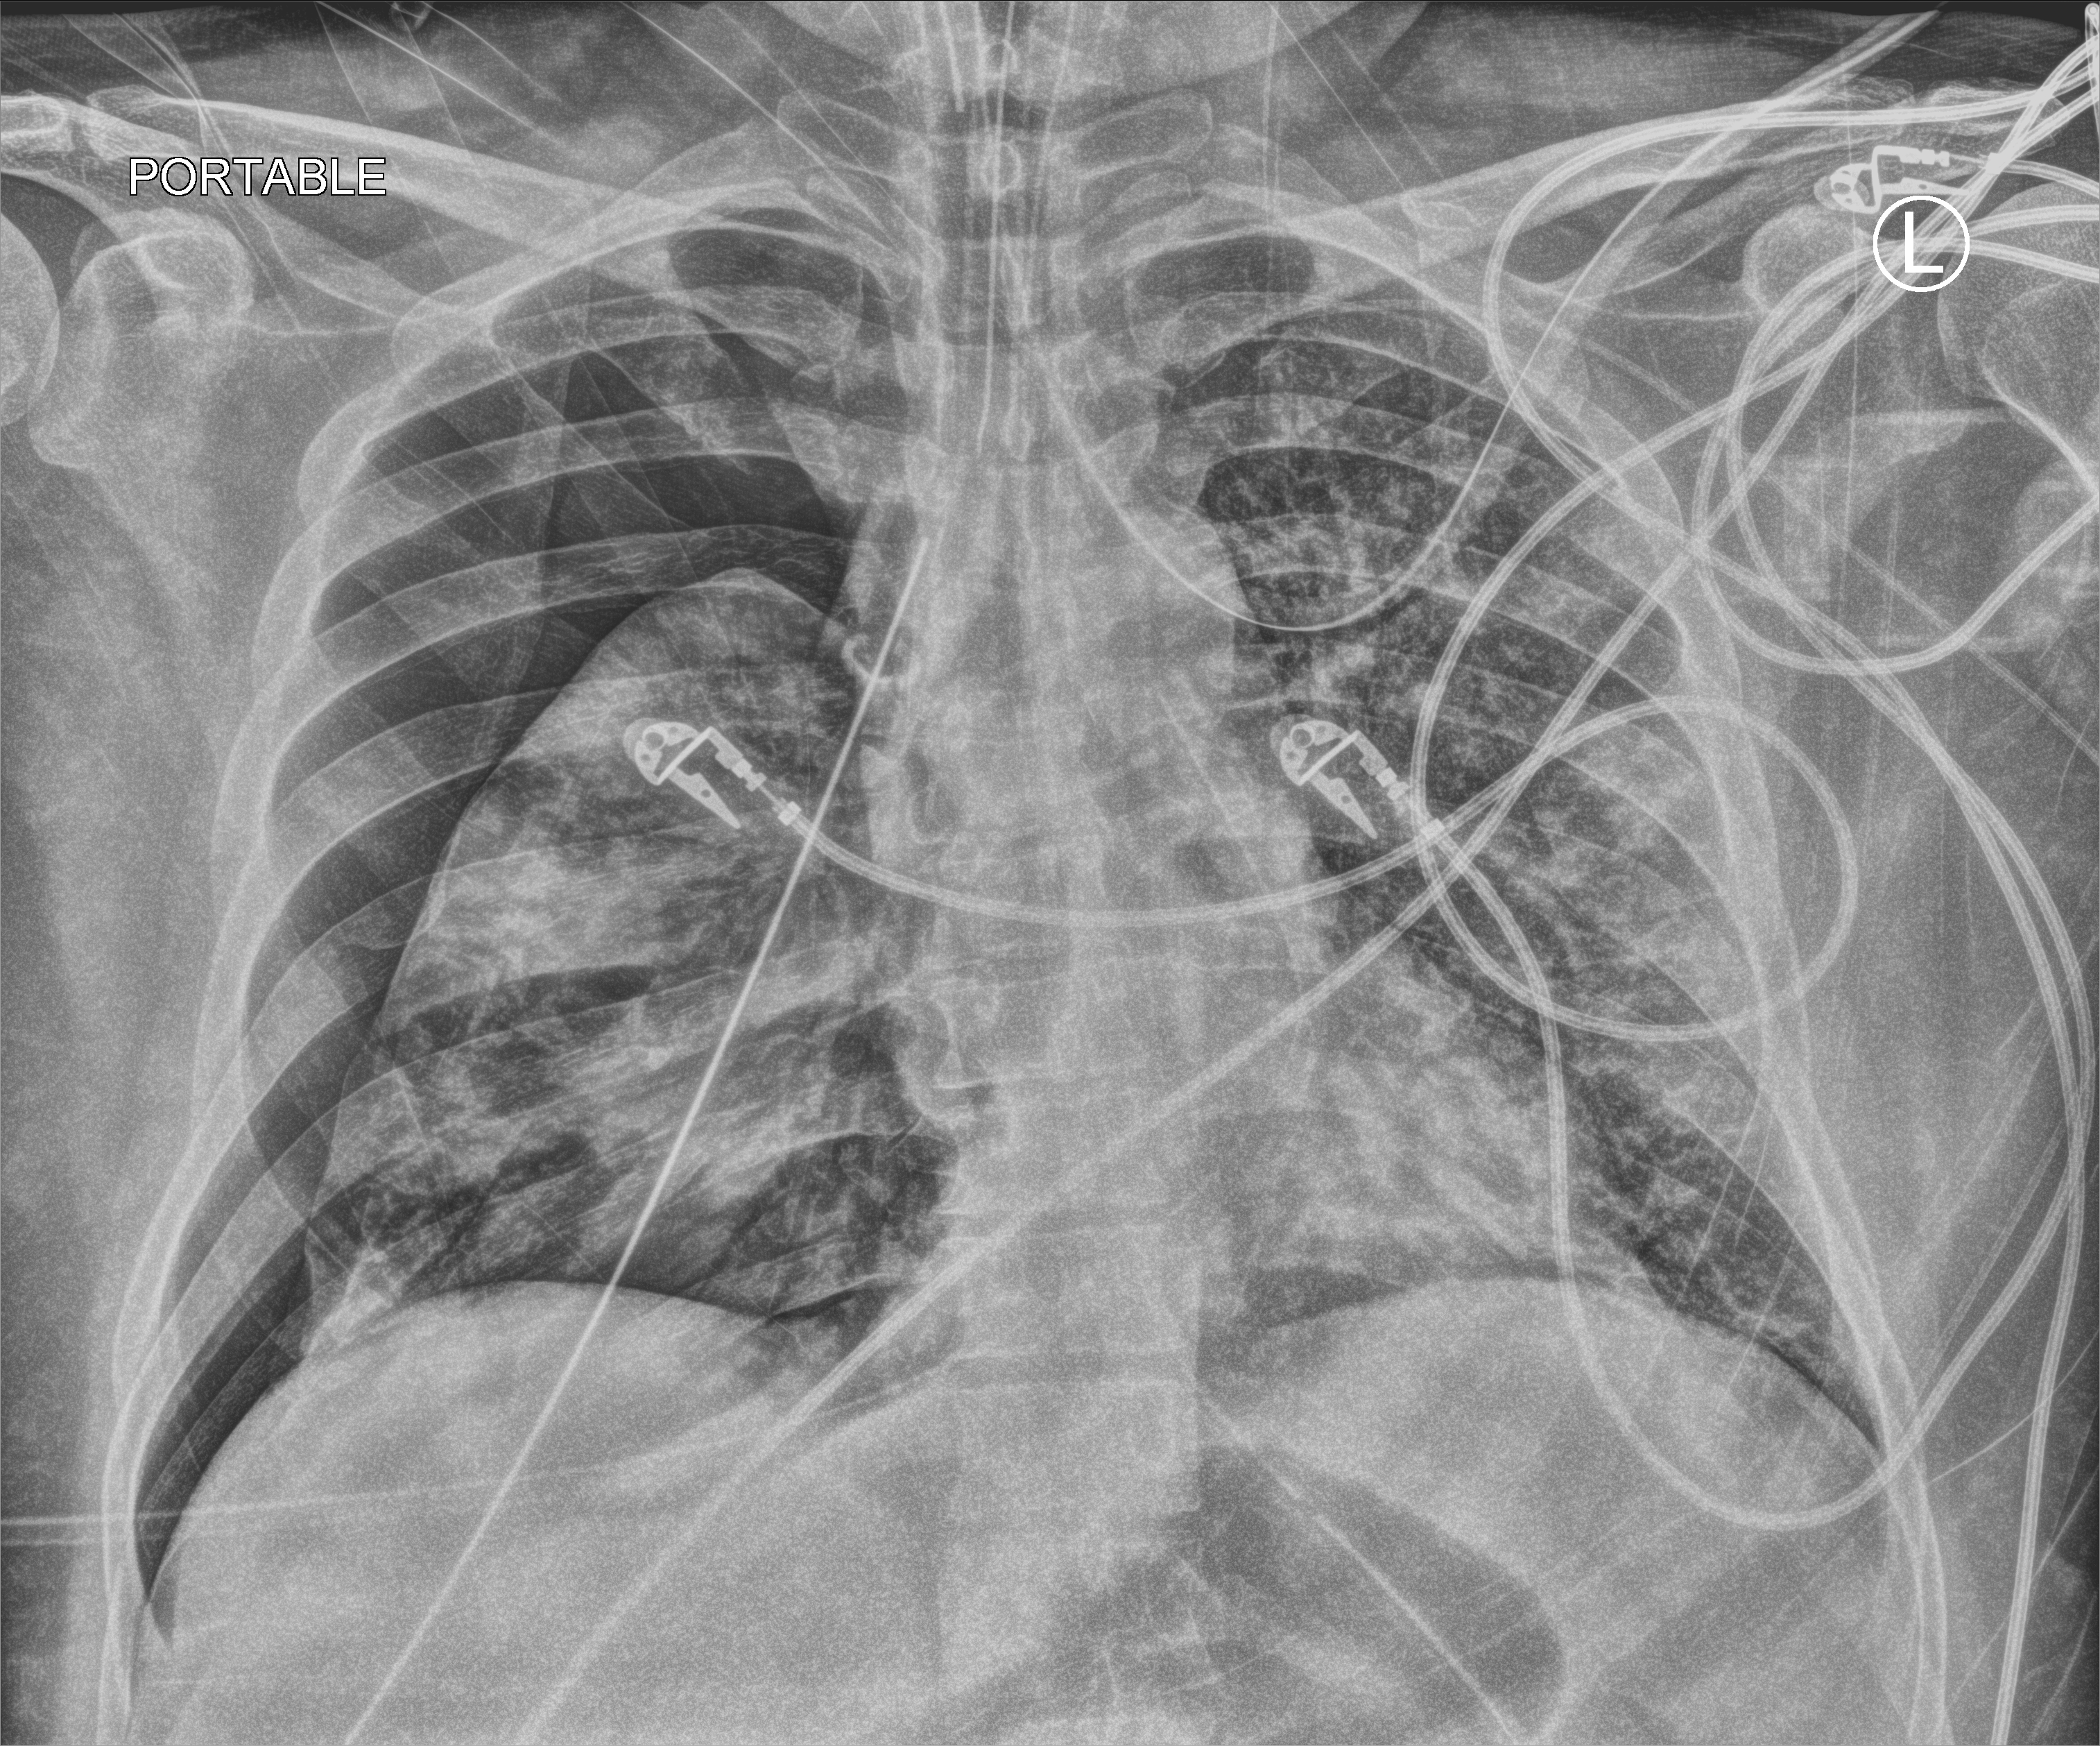
Portable chest radiograph; anteroposterior (AP) projection. Male patient hospitalised with COVID-19, age 18–59 years.
From the hospital-stay record, not from the radiograph (when in the stay this image was taken is not recorded): diabetes (admission record): yes; other chronic lung disease (admission record): no; admitted to intensive care during this hospital stay: yes.